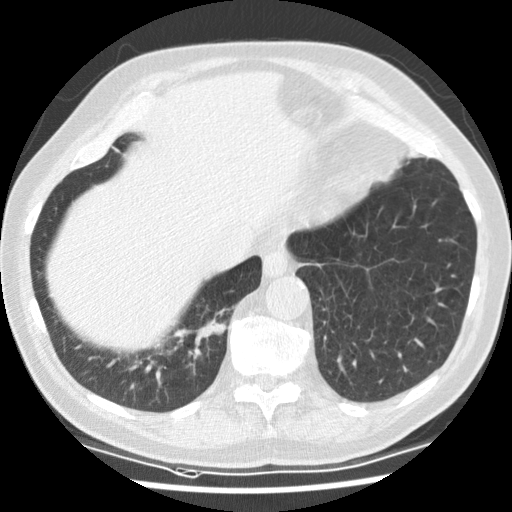
Low-dose screening chest CT, one axial slice; position 22 of 135 along the scan axis; 120 kVp; lung window (W 1500 / L -600 HU); 512 × 512 image matrix.
Annotated regions visible in this slice (manually delineated by an expert):
- lesion 2 (nodule, upper lobe of right lung): bounding box [x1, y1, x2, y2] px = [175, 310, 228, 368]